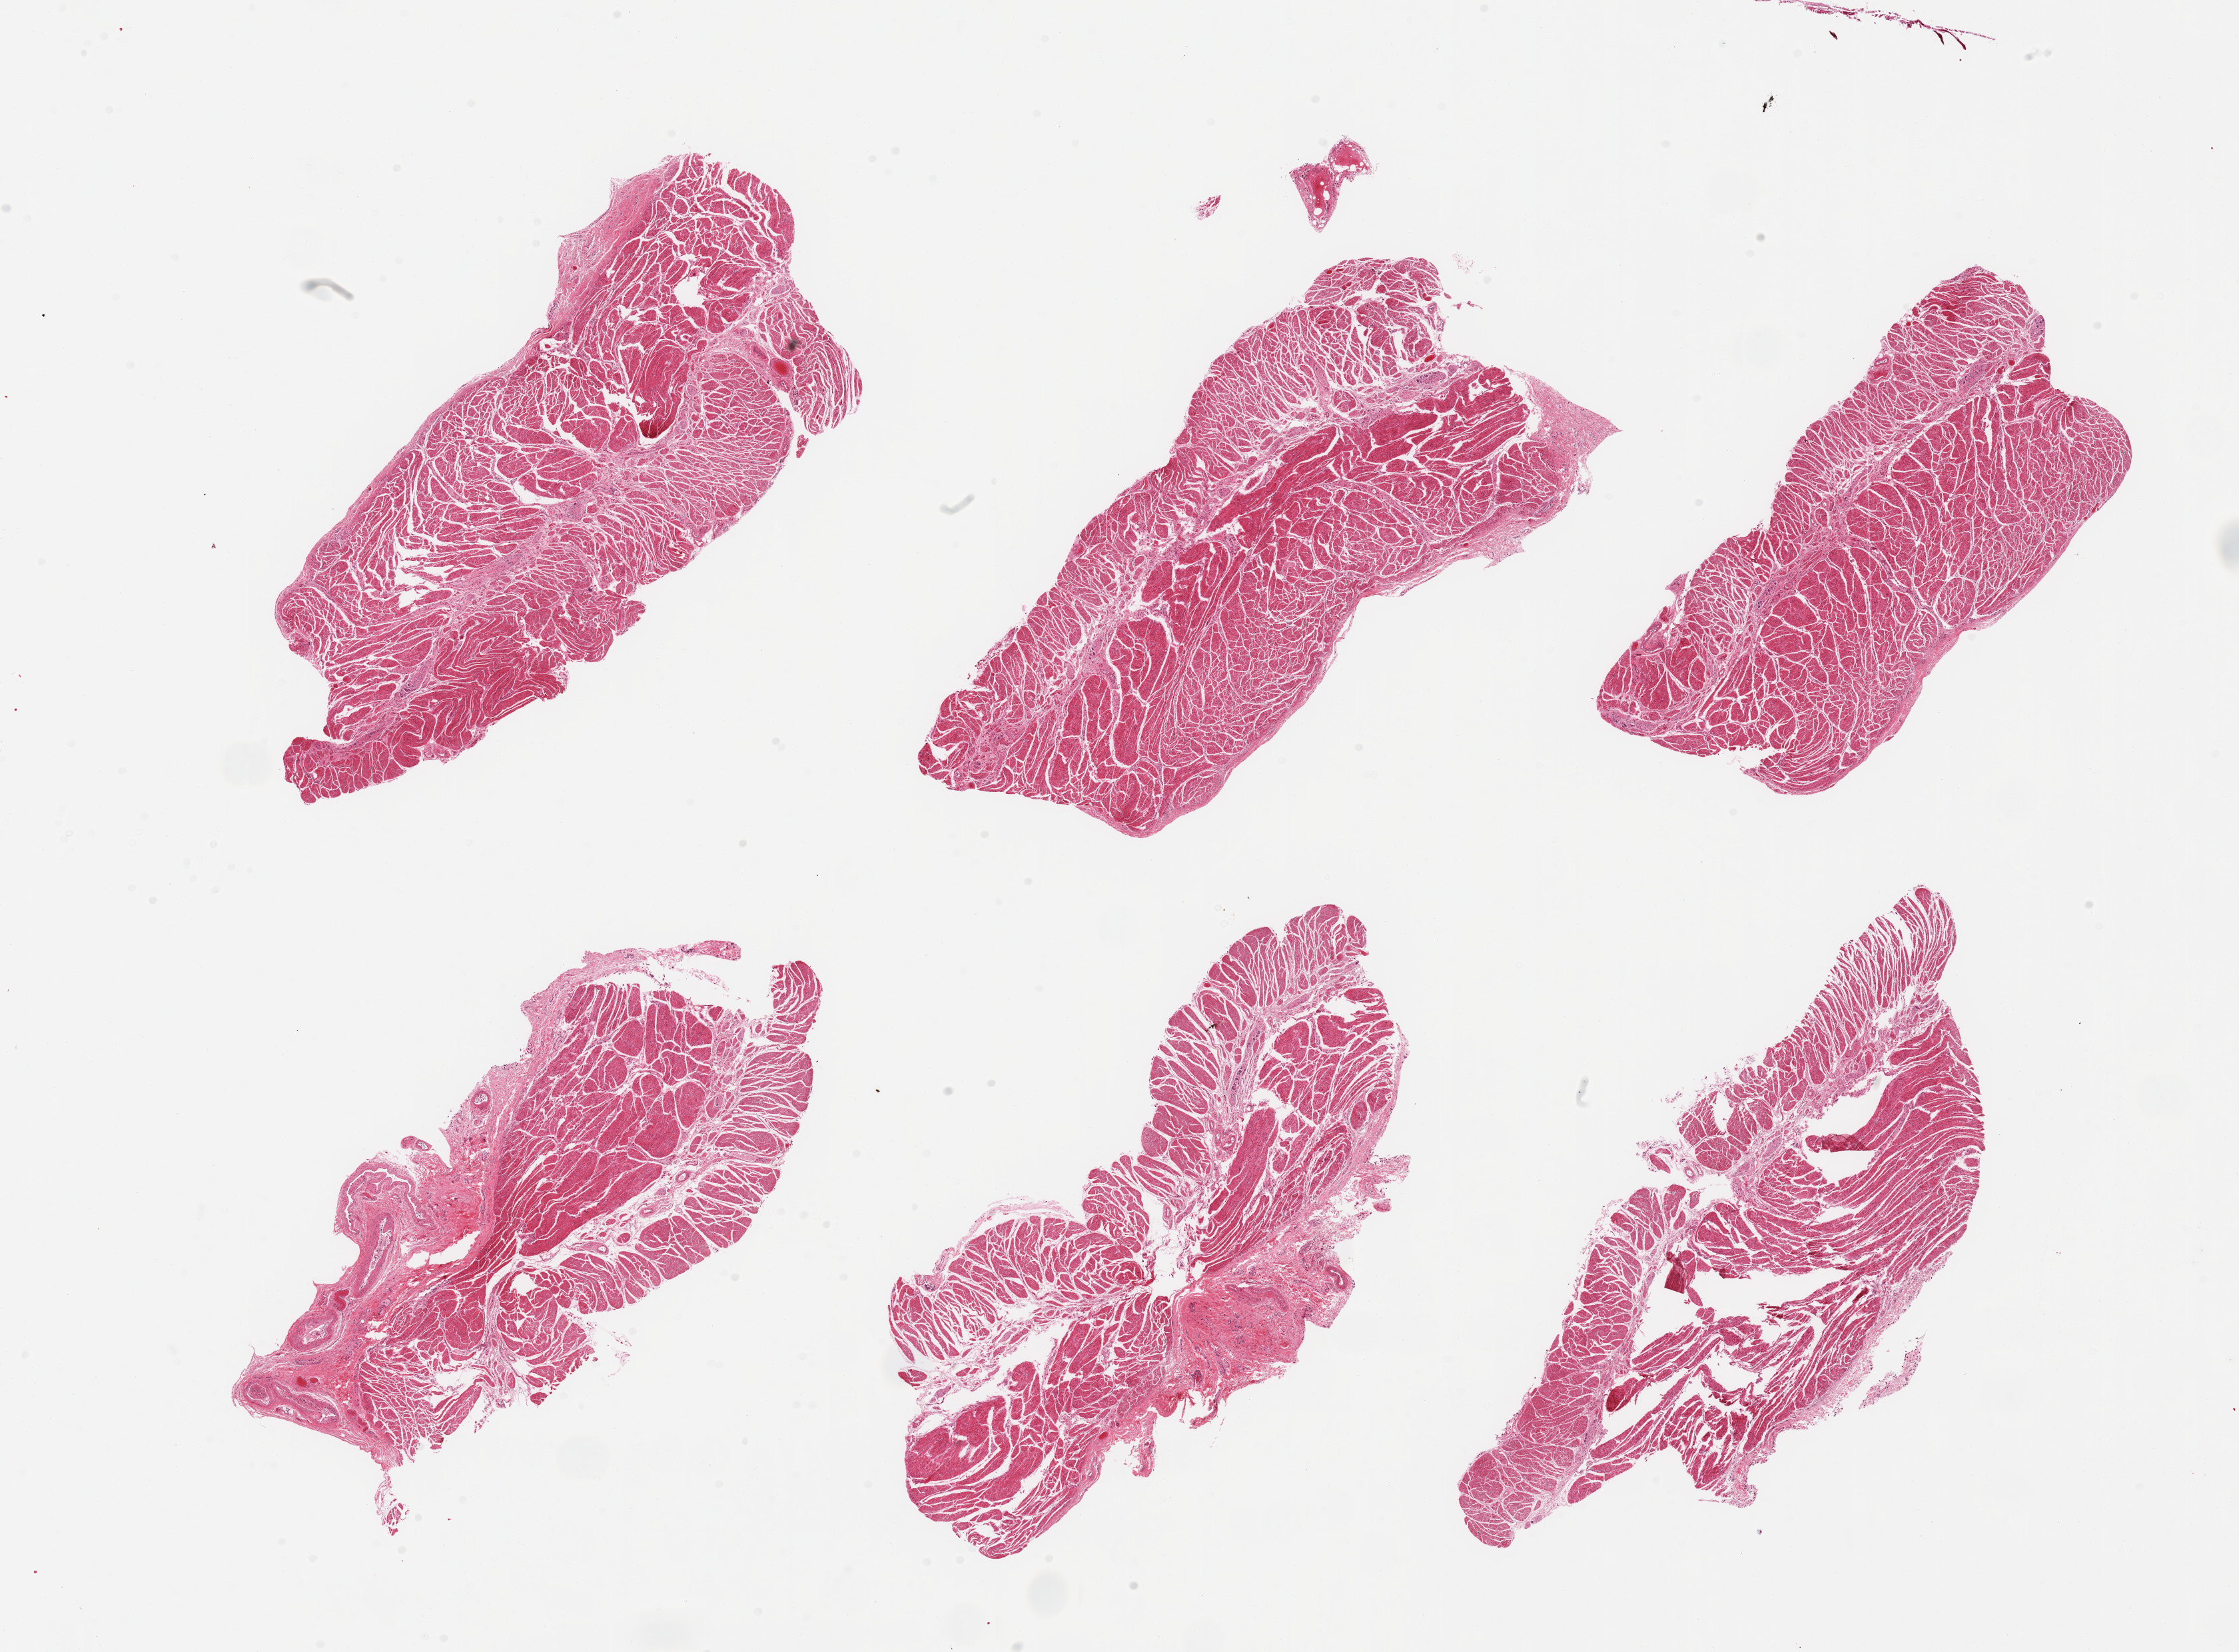
Whole-slide image, H&E stain, brightfield, shown as a low-resolution overview of the whole scanned area (about 26.6 x 19.6 mm, from a 20x scan). PAXgene-fixed, paraffin-embedded tissue. Sampled site (target tissue): esophageal muscle. Donor tissue sample.
Pathologist's review note for this sample: 6 pieces, confirmed target muscularis.